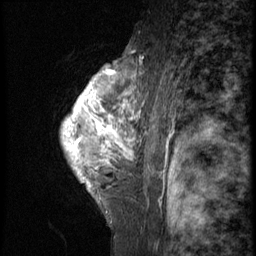
Breast MRI (dynamic contrast-enhanced), one sagittal slice. Position 44 of 58 along the scan axis. 3 images stored at this slice position (order not interpretable as contrast timing). 1.5 T. TE 4.2 ms, TR 9 ms. 2.5 mm slice thickness. 256 × 256 image matrix. Patient: female, 50 years. From the clinical record (not read from this slice): setting: breast cancer imaged before/during neoadjuvant chemotherapy; receptor status: triple-negative.
Annotated regions visible in this slice (semi-automatic segmentation, software-assisted and operator-edited):
- analysis volume of interest (the breast-tissue region the enhancement analysis was run in; not a lesion): bounding box [x1, y1, x2, y2] px = [61, 48, 128, 214]
- tumour enhancement mask (voxels above the 140 % enhancement threshold inside the analysis volume of interest): [66, 64, 128, 186]